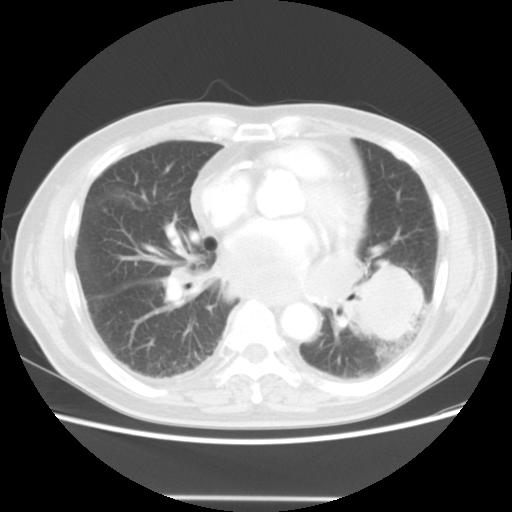
Chest CT, one axial slice; slice 22 of 56 in the series (ordered by position); reconstruction kernel STANDARD; lung window (W 1500 / L -600 HU); 5 mm slice thickness; 512 × 512 image matrix, field of view 360 × 360 mm. Patient: male, 66 years. From the clinical record (not read from this slice): clinical TNM (as recorded): T4 N3 M0; histopathological grade: G3.
Structures marked on this image (rectangle marked by the reading radiologist):
- lung tumour (recorded histology: small cell carcinoma): bounding box (x1, y1, x2, y2) in pixels: (351, 248, 428, 356)